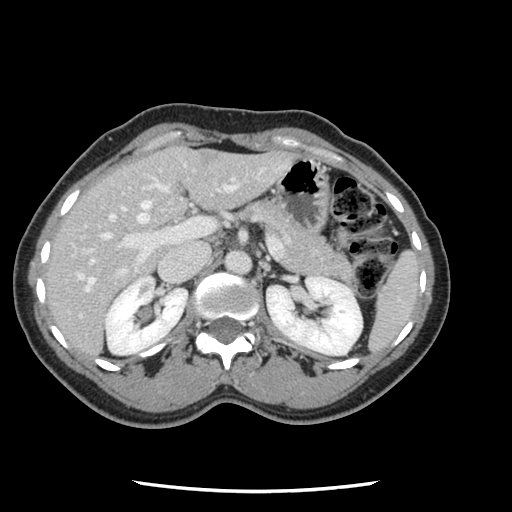
Contrast-enhanced abdominal CT, one axial slice. Slice 69 of 134 in the series (ordered by position). 120 kVp. Intravenous contrast given. Soft-tissue window (W 400 / L 40 HU). 2.5 mm slice thickness. 512 × 512 image matrix, field of view 330 × 330 mm. Female patient, age 43 years. Case-level facts recorded for this patient, not image findings: diagnosis: colorectal cancer liver metastases, imaged before liver resection; multiple liver metastases: yes; largest metastasis: 3.4 cm; disease in both lobes: yes.
Outlined on this slice (expert manual segmentation):
- hepatic veins: bounding box (x1, y1, x2, y2) in pixels: (78, 180, 235, 291)
- liver: (47, 147, 293, 356)
- planned liver remnant (the part of the liver to remain after resection): (47, 150, 186, 303)
- portal vein (with intrahepatic branches): (72, 177, 235, 279)
- liver metastasis: (203, 156, 218, 162)